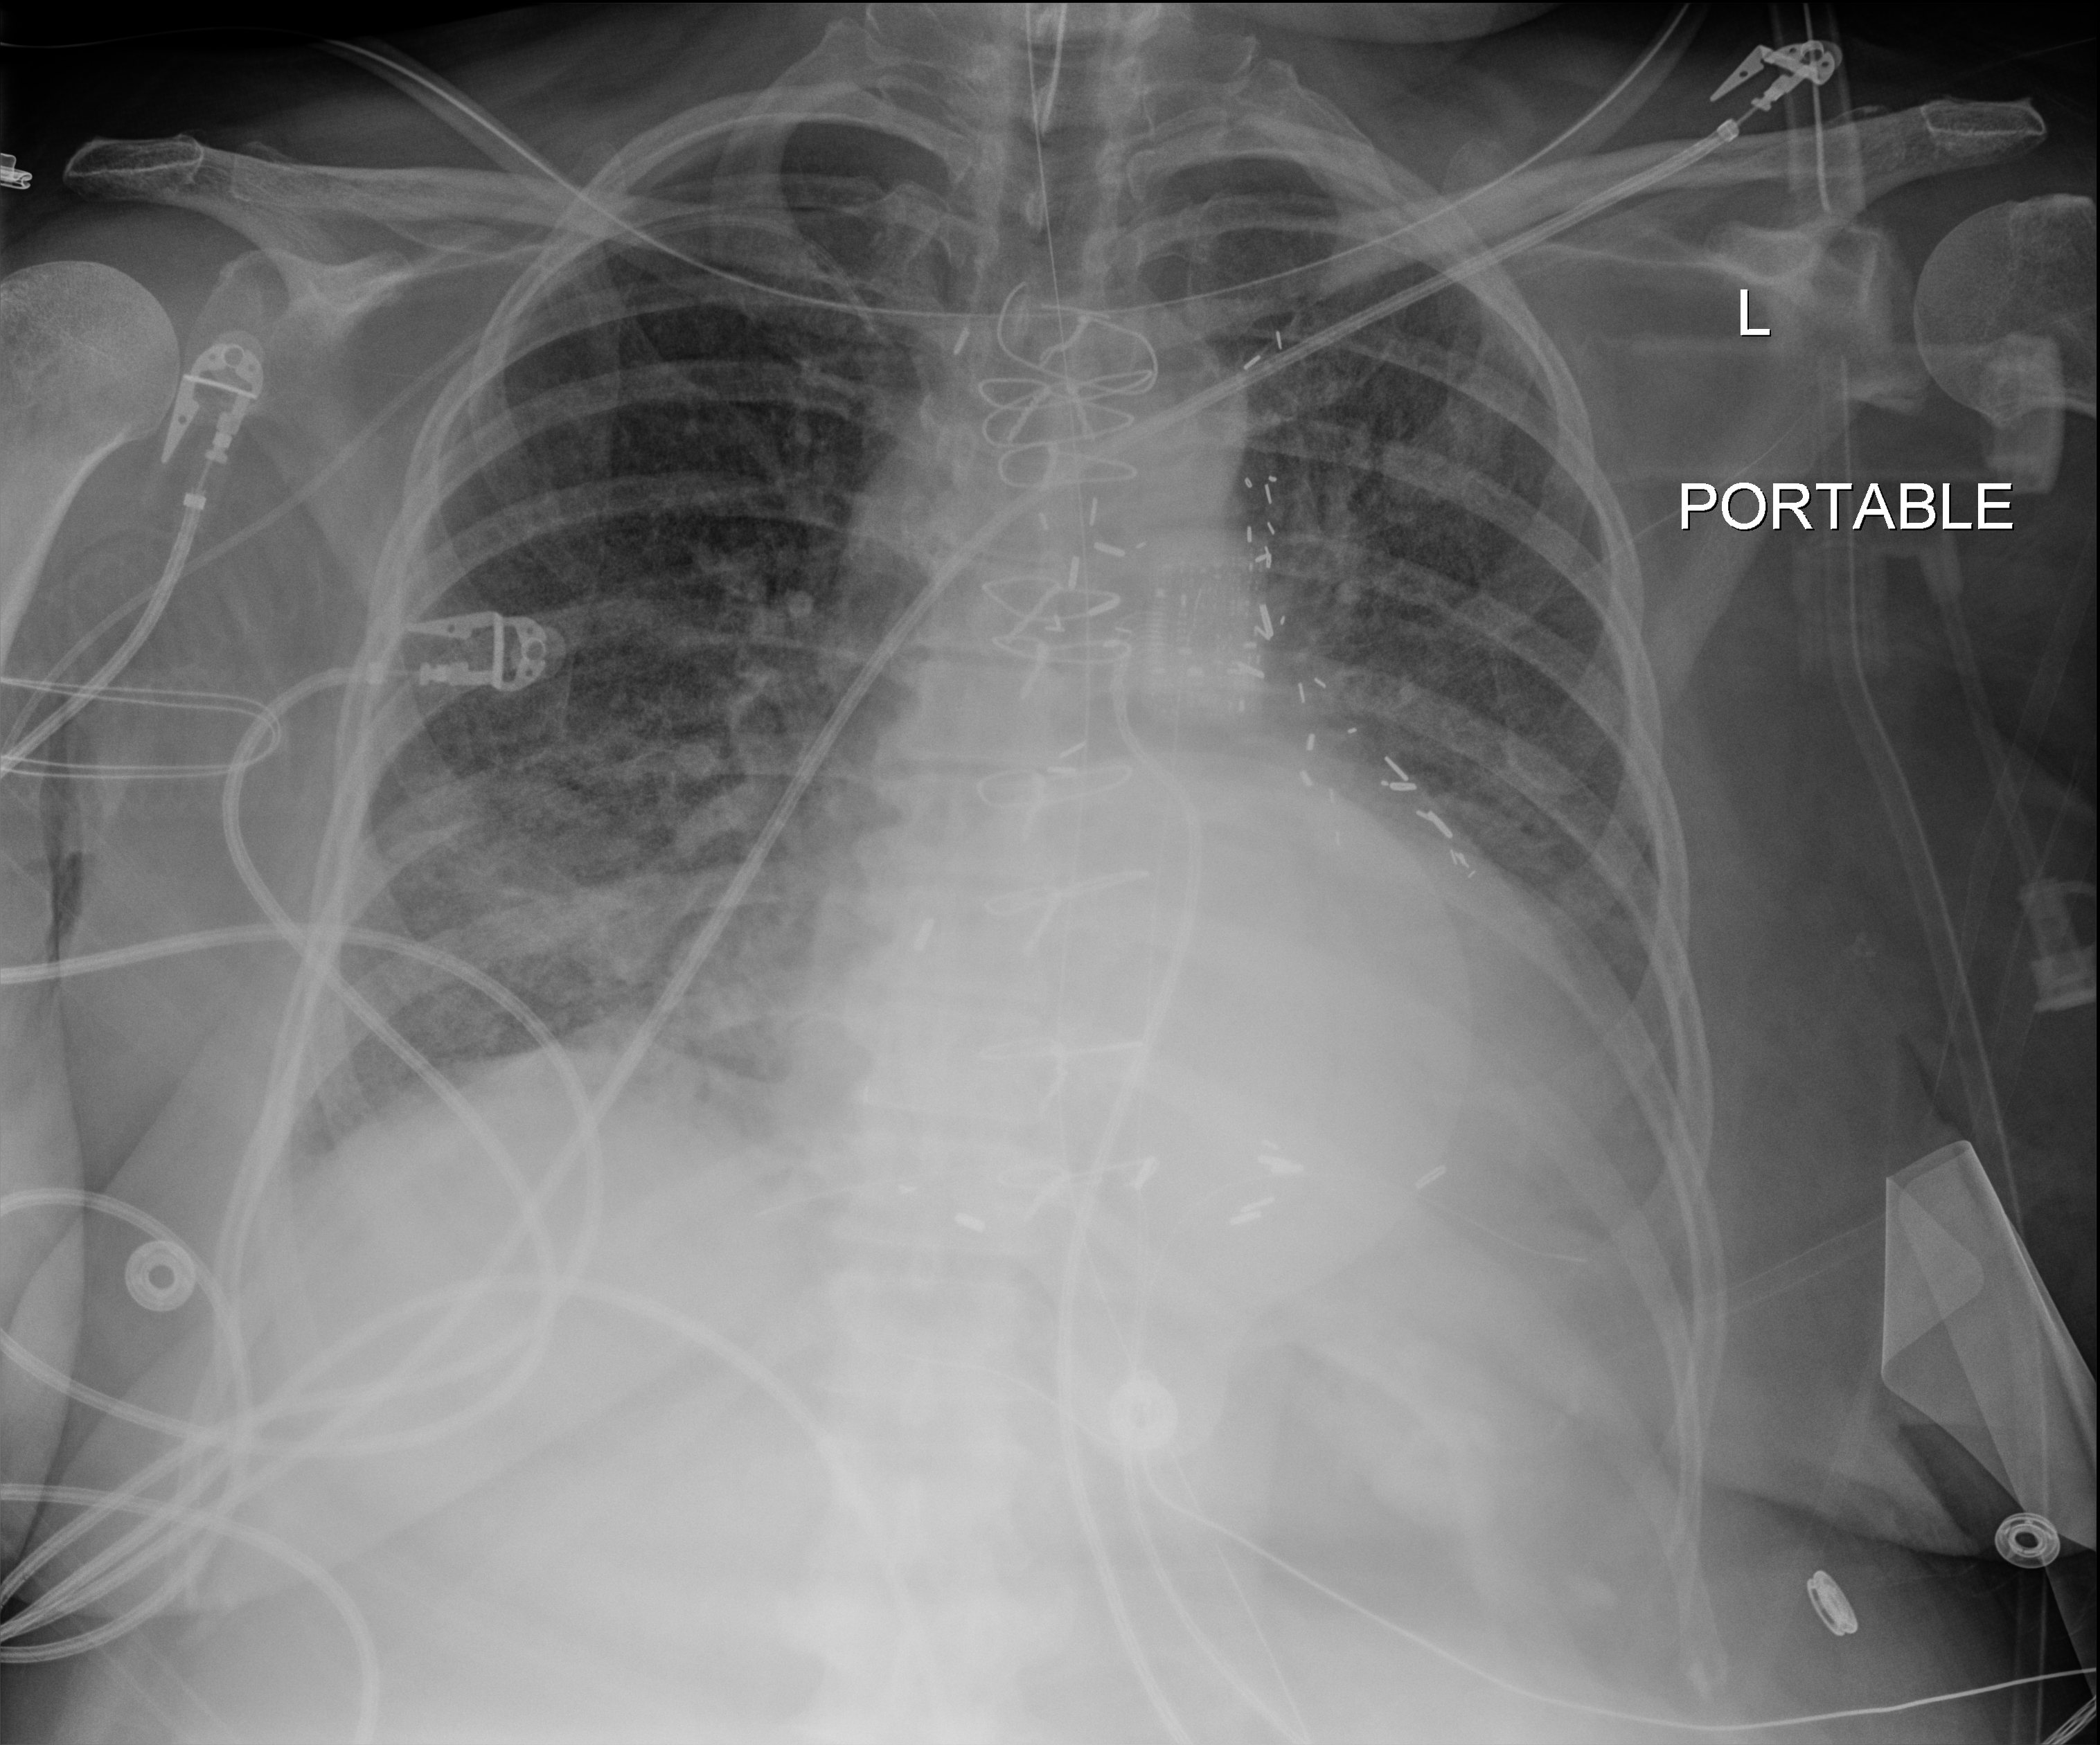
Chest X-ray (portable); anteroposterior (AP) projection. Patient hospitalised with COVID-19; female, aged 60–74 years.
Hospital-stay facts (about this admission, not read from this image; timing relative to this image not recorded):
- diabetes (admission record): no
- mechanically ventilated during this hospital stay: yes